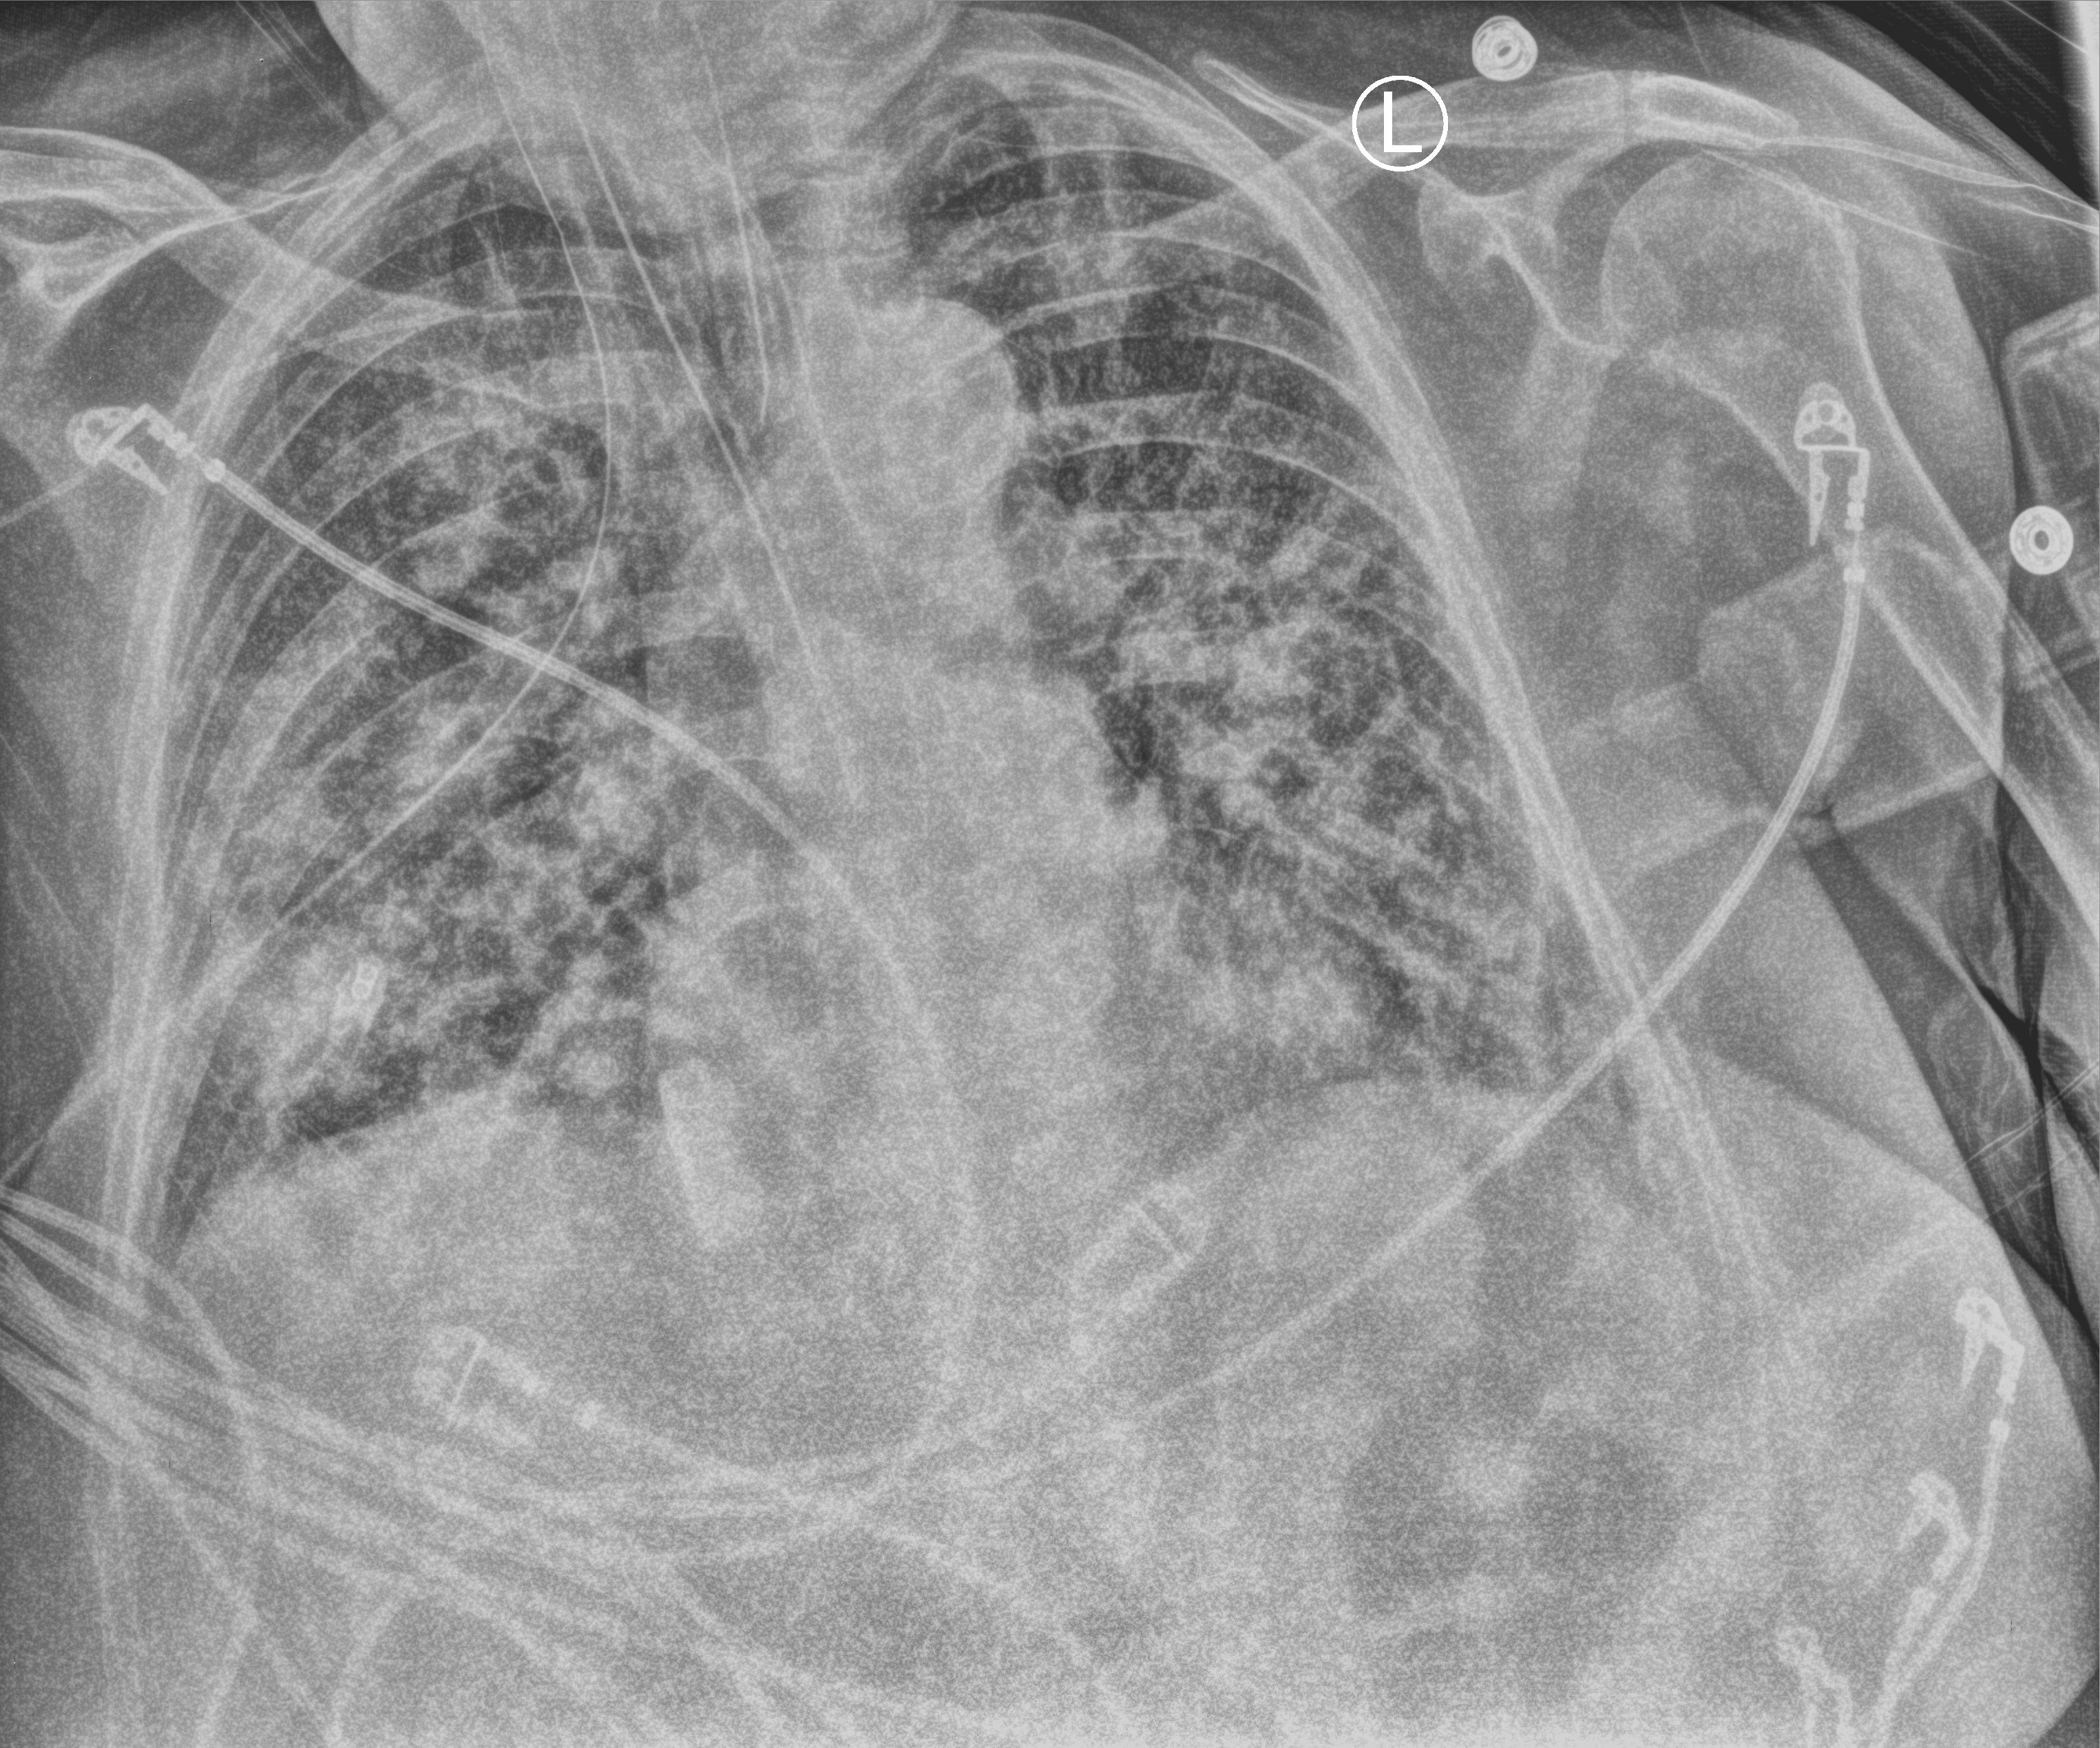
Chest X-ray (portable). Female patient hospitalised with COVID-19, age 60–74 years.
Admission-level facts for this patient (not findings on this image; timing relative to this image not recorded):
- admitted to intensive care during this hospital stay: yes
- length of hospital stay: 19 days
- mechanically ventilated during this hospital stay: yes